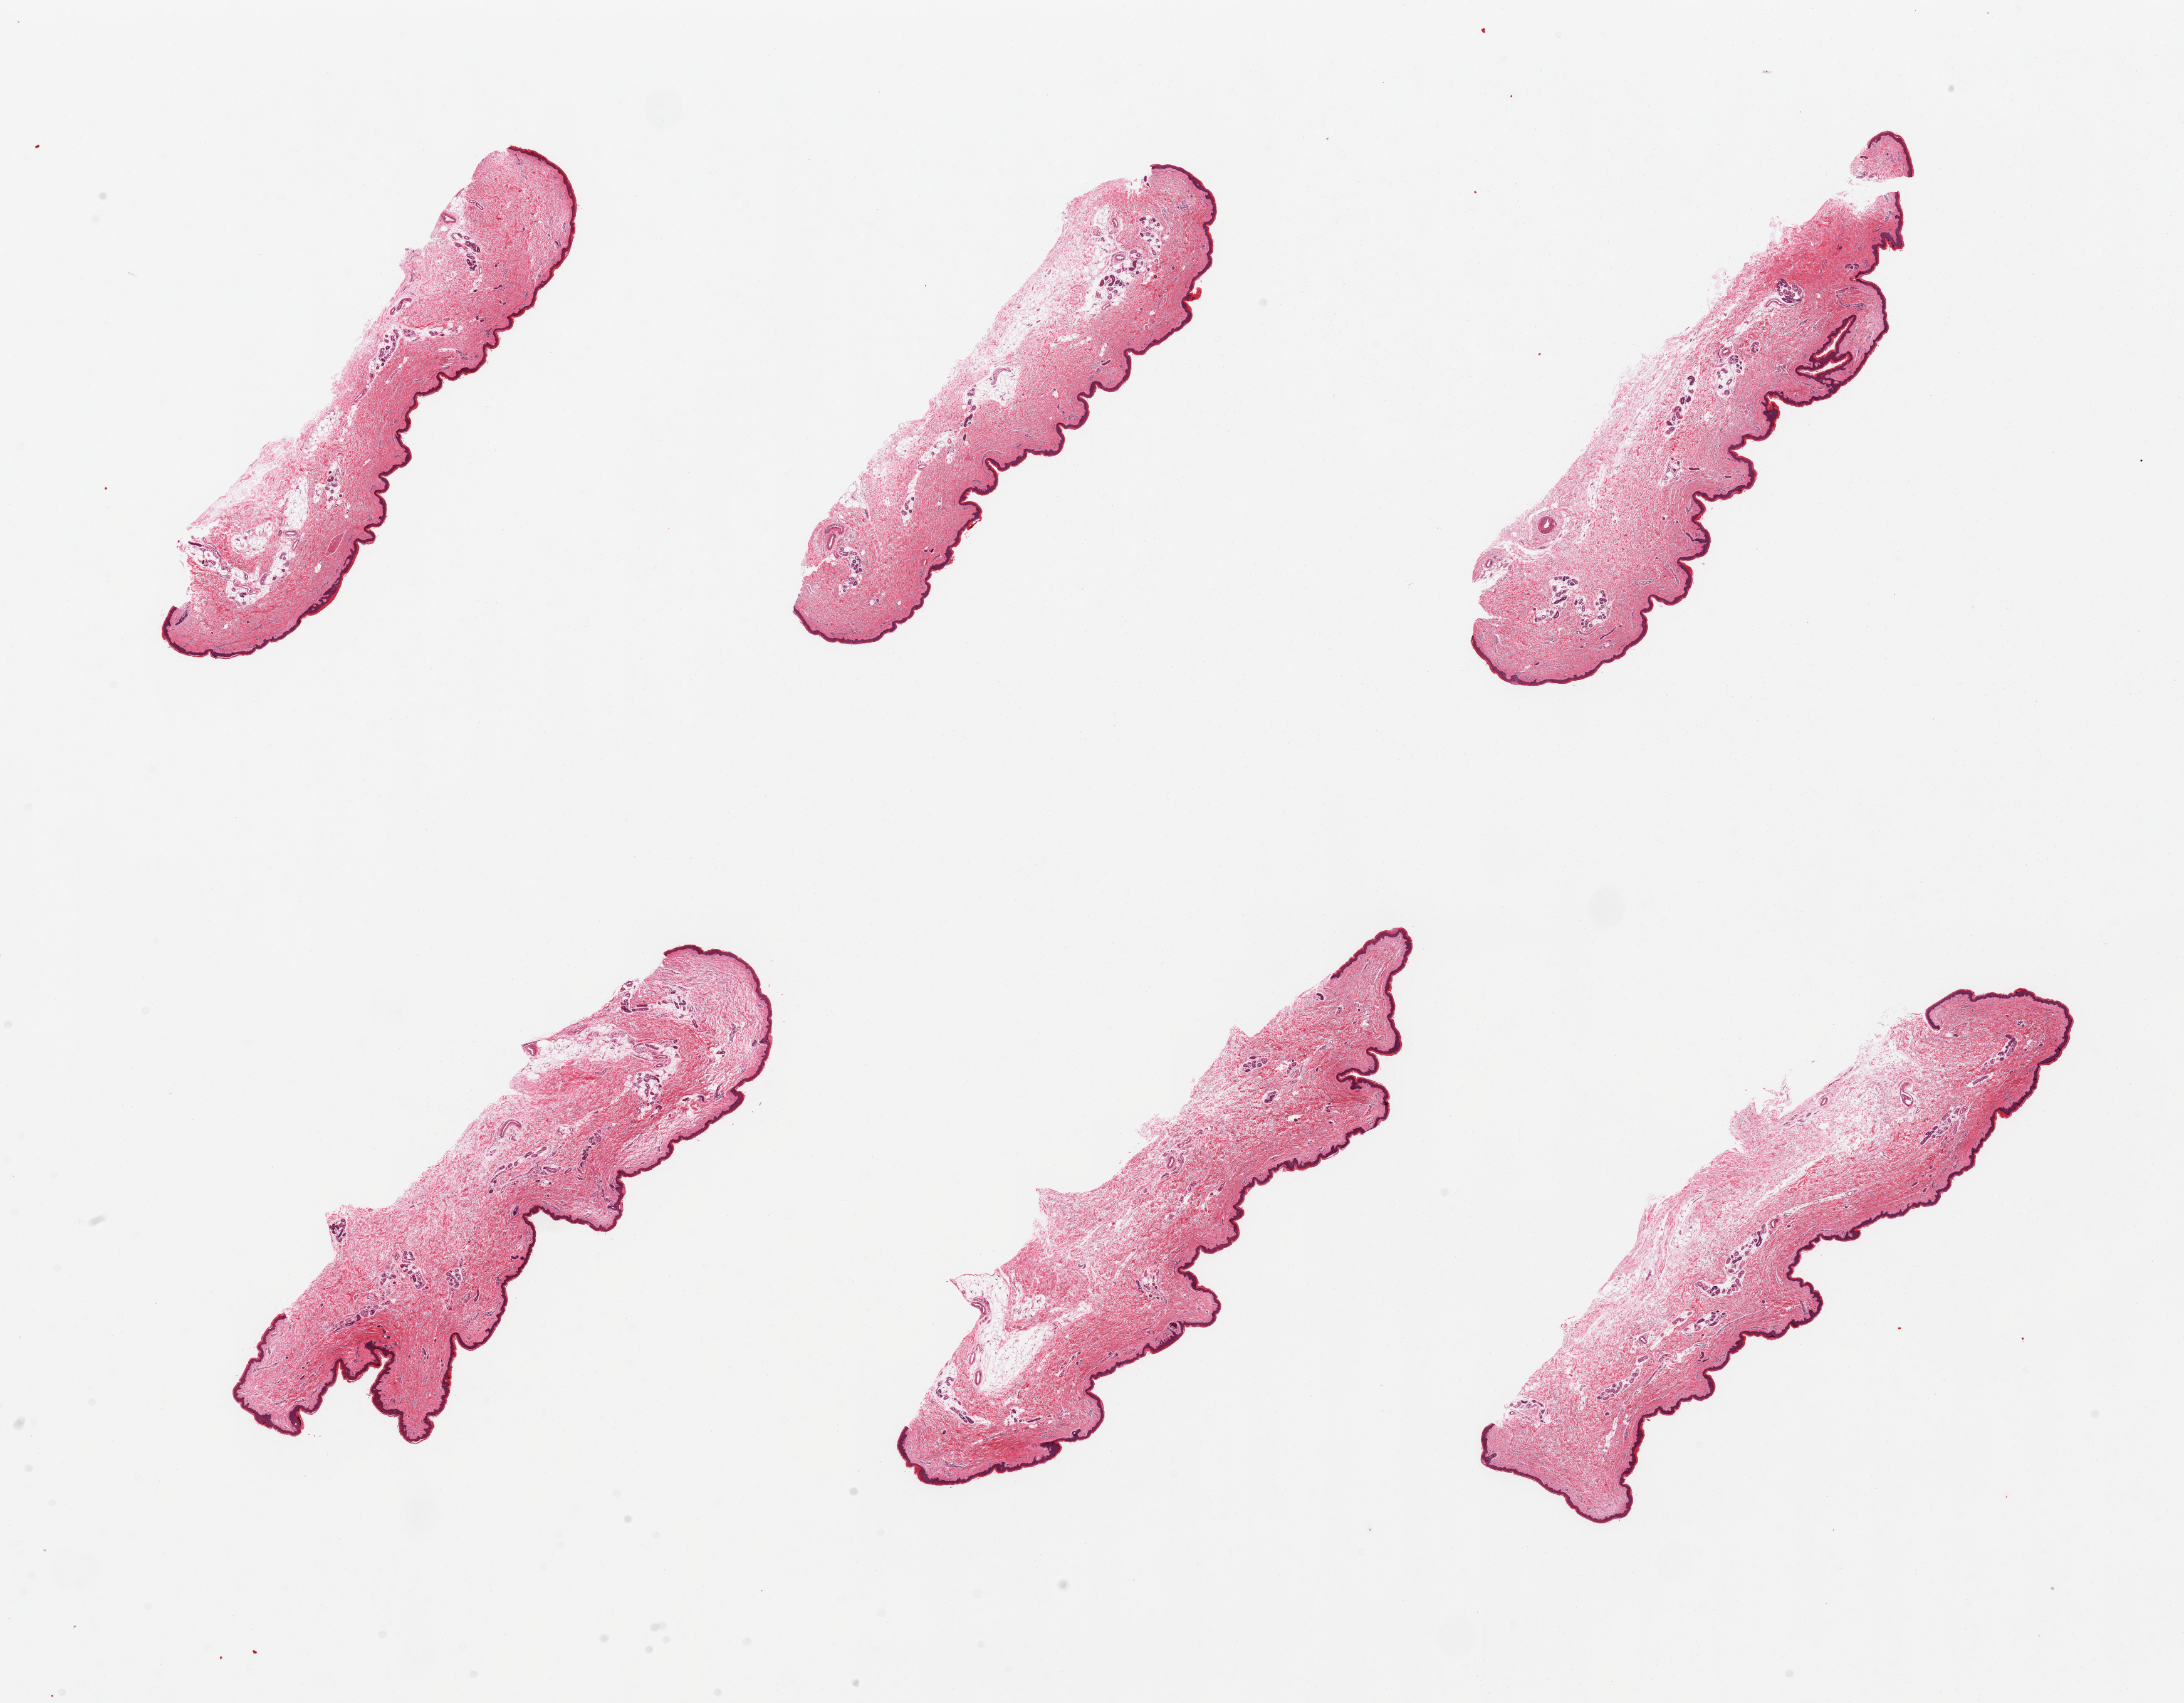
H&E whole-slide image, shown as a low-resolution overview of the whole scanned area (about 27.6 x 21.5 mm); PAXgene-fixed, paraffin-embedded tissue; sampled site (target tissue): skin of lower leg; donor tissue sample.
Reviewer comment on this tissue sample: 6 pieces, minimal dermal fat; squamous epithelium is ~40 microns.